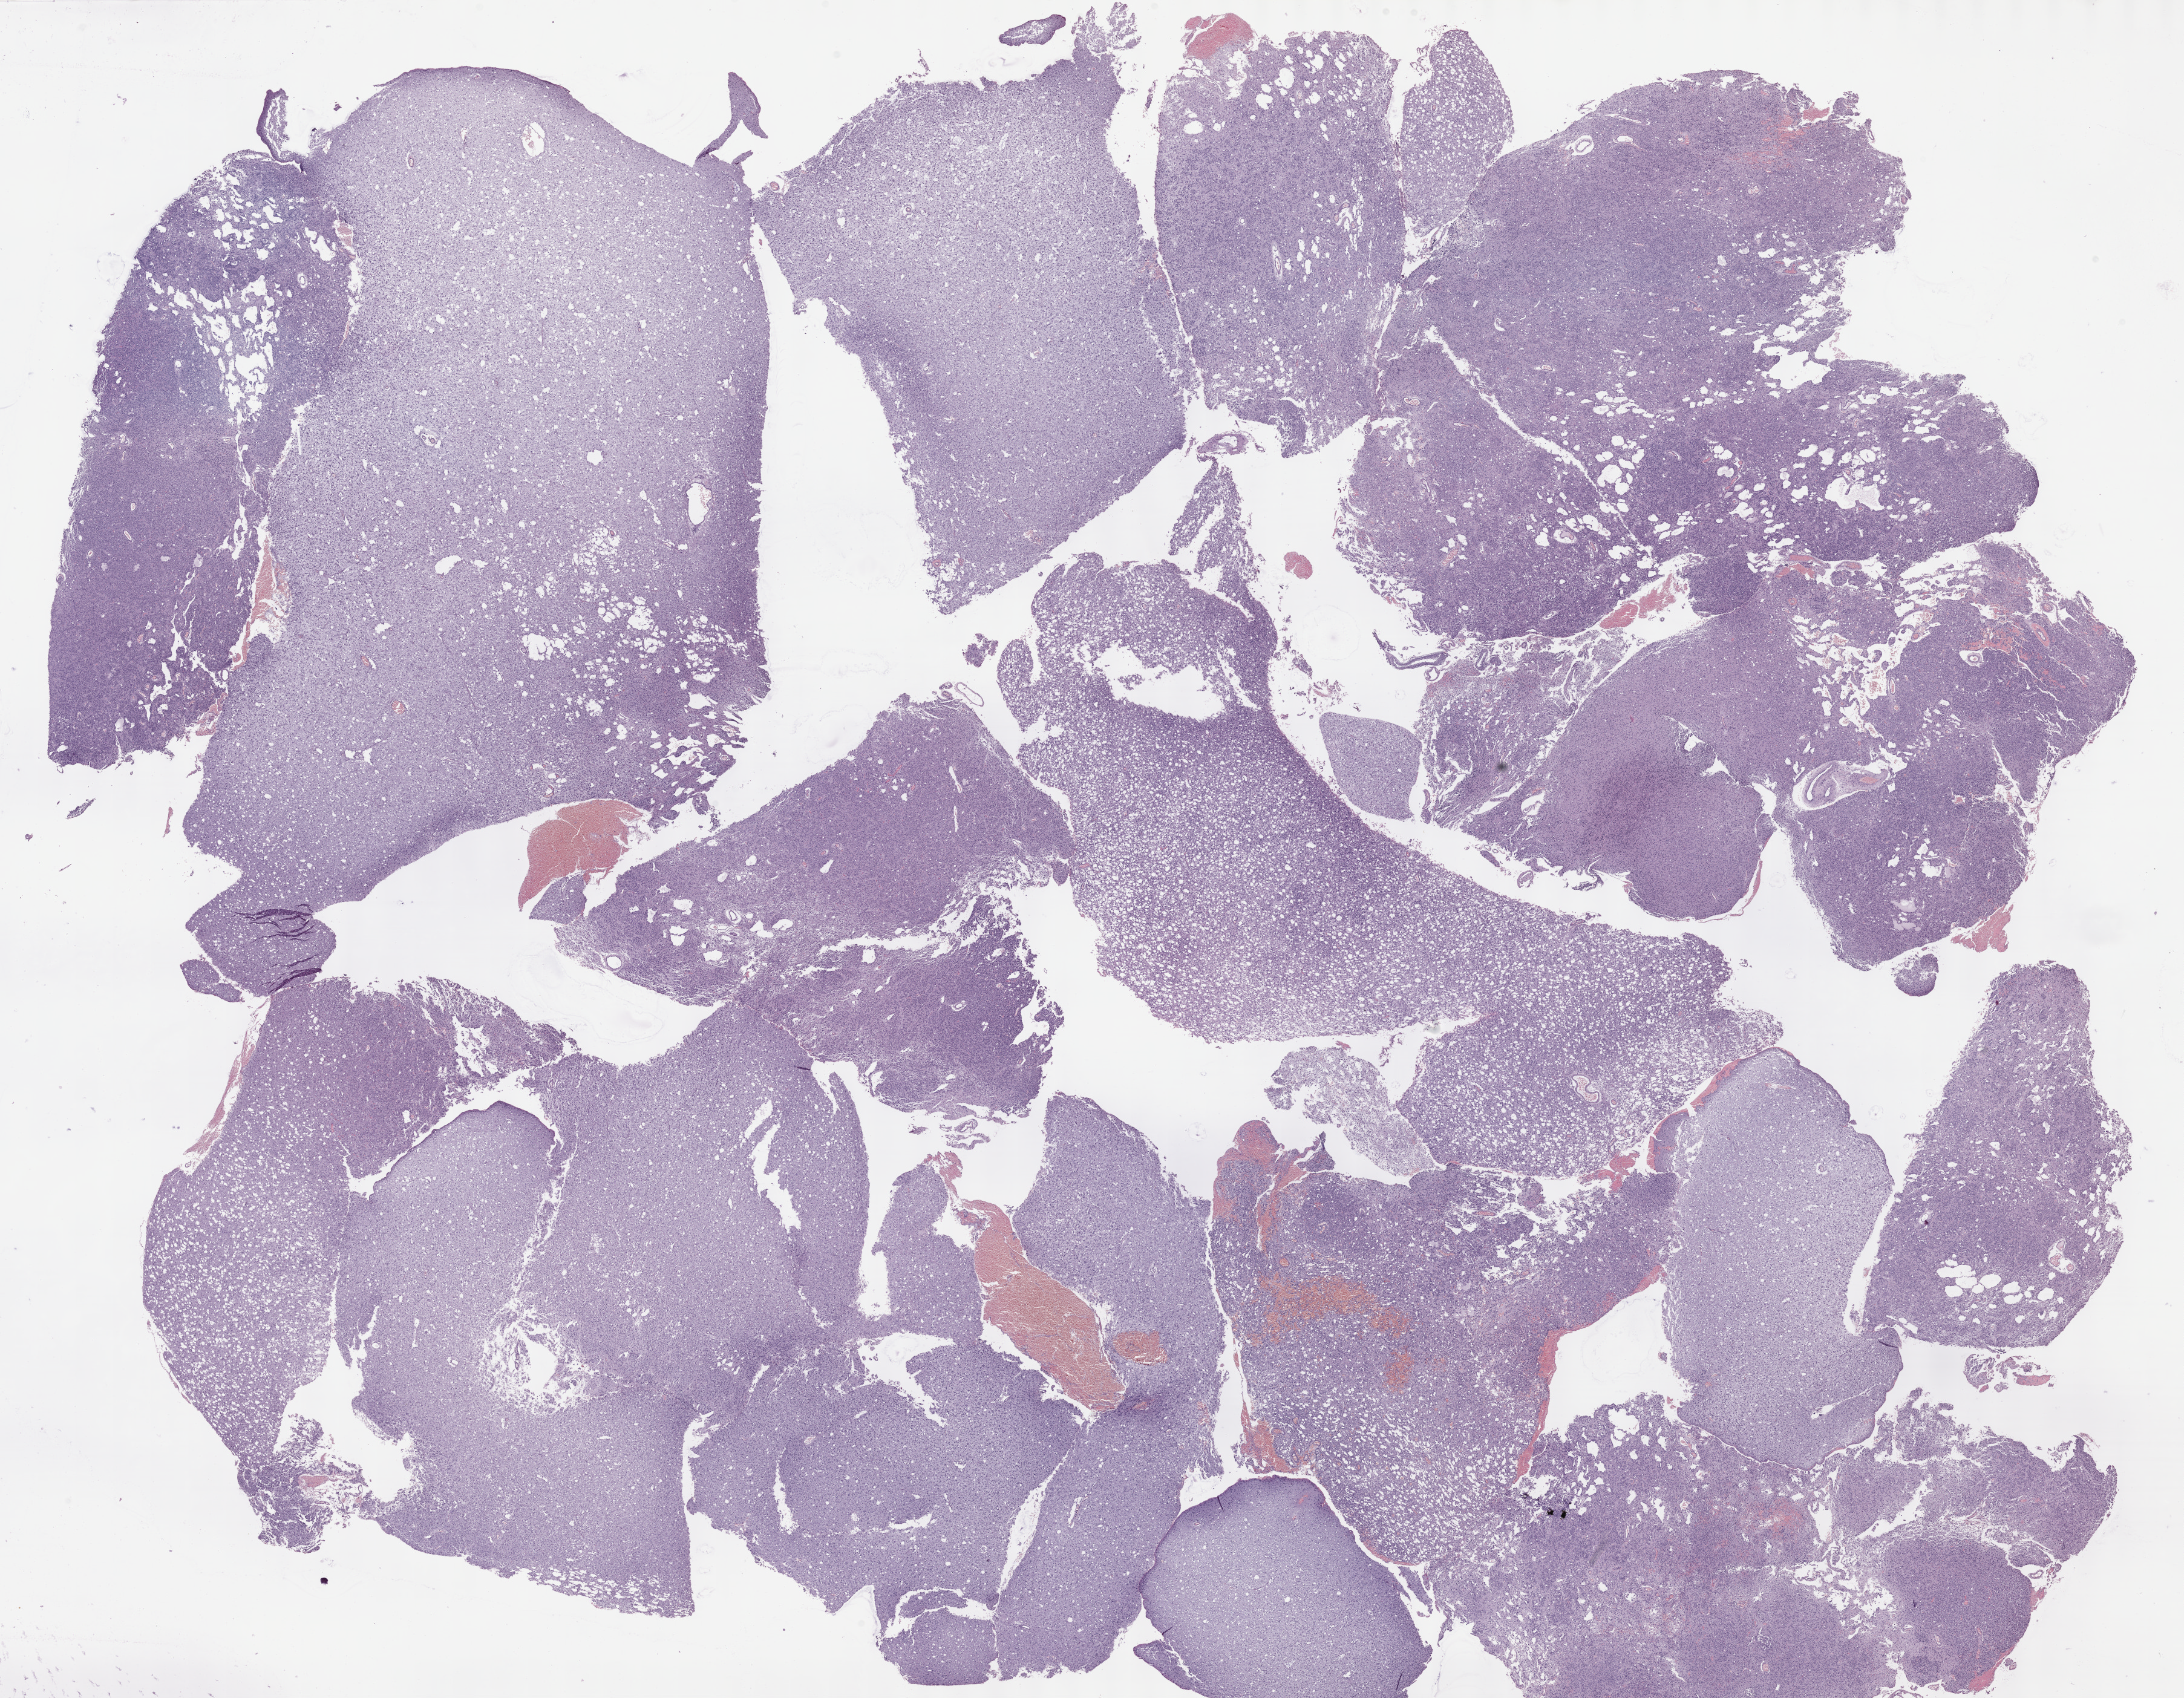
Whole-slide histology image, H&E, a low-resolution overview of the entire scanned area, about 29.2 x 22.7 mm (slide scanned at 40x). FFPE section. Sample: primary tumour, brain. Male, age 22 years at initial diagnosis. Histologic grade: G3 (poorly differentiated).
- diagnosis: Mixed glioma (cerebrum)
- laterality: right